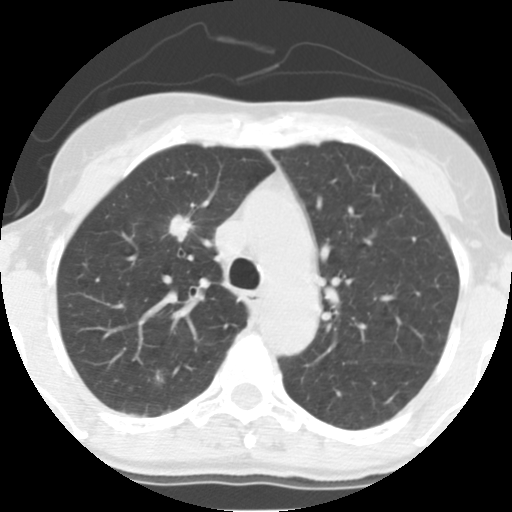
Low-dose screening chest CT, one axial slice; position 98 of 140 along the scan axis; reconstruction kernel STANDARD; 140 kVp; lung window (W 1500 / L -600 HU); 2.5 mm slice thickness; 512 × 512 image matrix, field of view 280 × 280 mm.
Structures marked on this image (outlined manually by an expert reader):
- lesion 1 (tumor, upper lobe of right lung): bounding box [x1, y1, x2, y2] px = [169, 214, 193, 241]